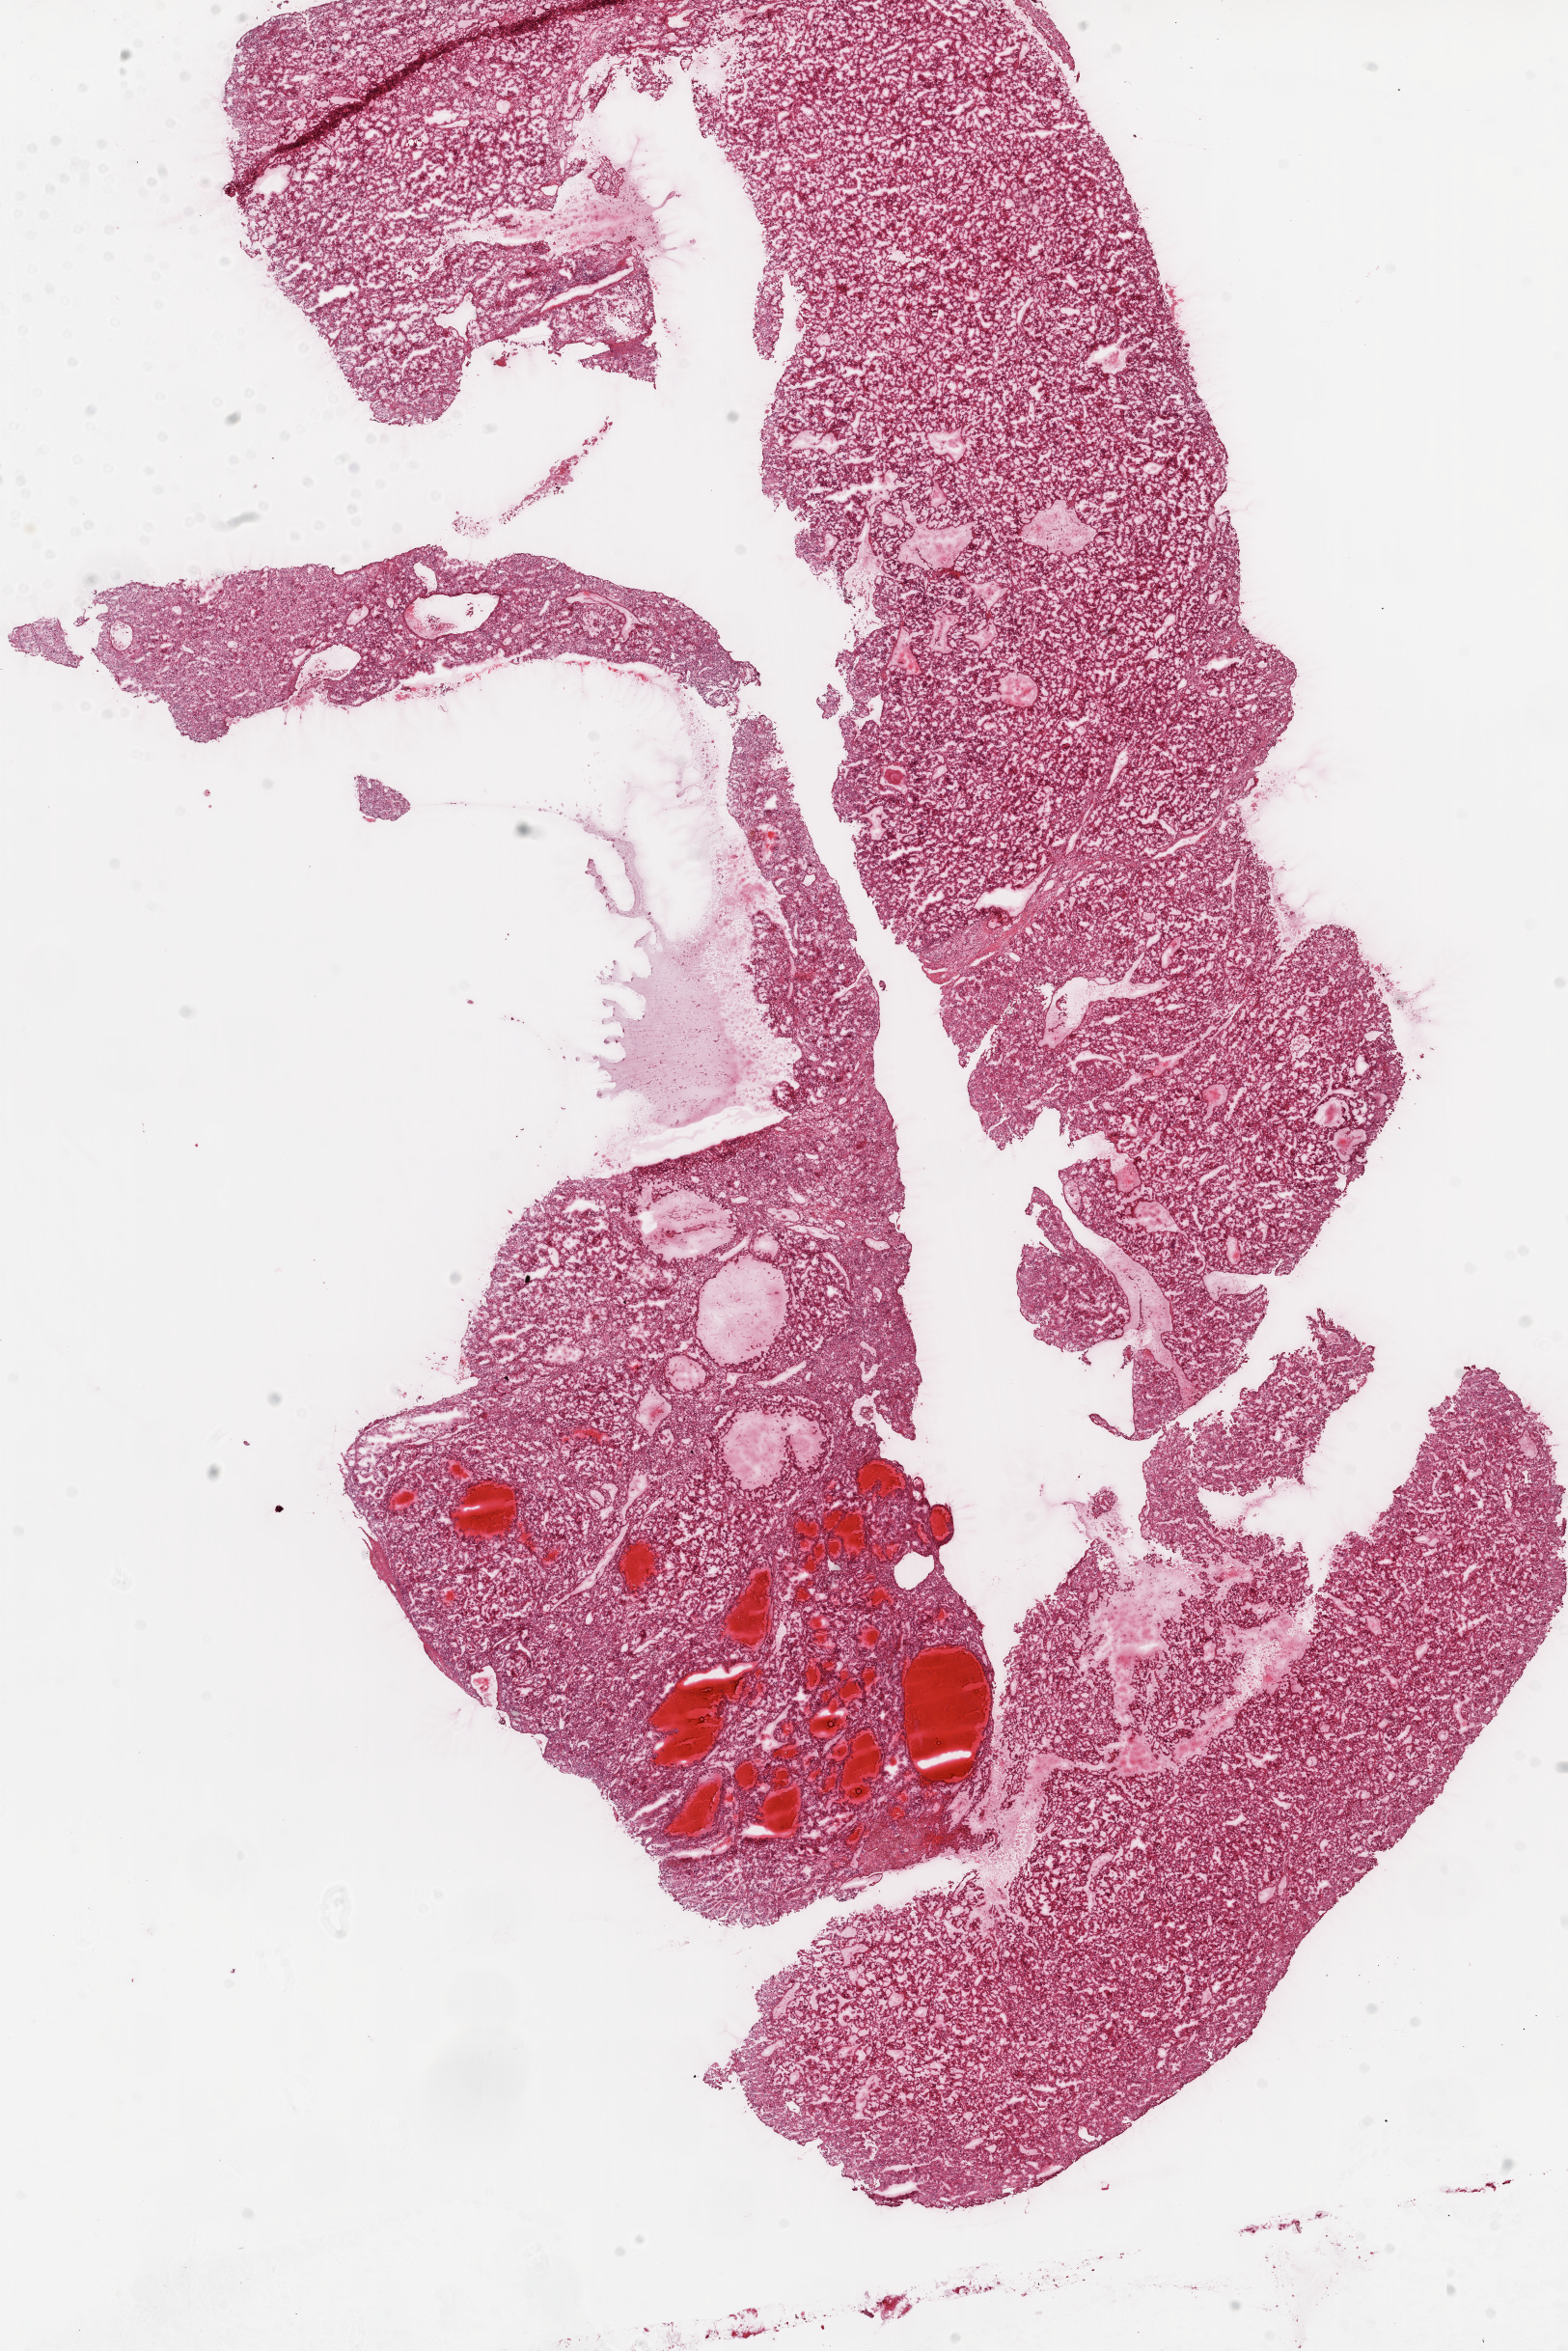
Digitized H&E tissue section (whole slide) — low-resolution overview of the scanned area, about 13.0 x 19.5 mm, frozen section from the top of the tissue portion, sample: primary tumour, kidney. Male, age 56 years at initial diagnosis. Histologic grade: G3 (poorly differentiated). Slide review estimates, as recorded: tumour cells 95%, tumour nuclei 90%, normal cells 0%, stromal cells 5%, necrosis 0%.
Laterality: right. Diagnosis: Clear cell adenocarcinoma, NOS. AJCC pathologic stage: I.